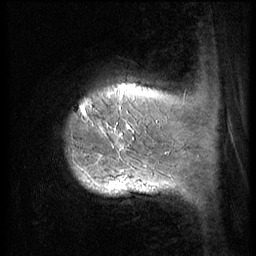
Breast MRI (dynamic contrast-enhanced), one sagittal slice; slice 8 of 56 in the series (ordered by position); 3 images stored at this slice position (order not interpretable as contrast timing); 1.5 T; TE 4.2 ms, TR 9 ms; 256 × 256 image matrix, field of view 180 × 180 mm. Patient: female, 49 years. From the clinical record (not read from this slice): setting: breast cancer imaged before/during neoadjuvant chemotherapy; receptor status: HER2-positive.
Structures marked on this image (semi-automatically segmented with operator editing):
- analysis volume of interest (the breast-tissue region the enhancement analysis was run in; not a lesion): box from (x=55, y=79) to (x=152, y=203) px
- tumour enhancement mask (voxels above the 140 % enhancement threshold inside the analysis volume of interest): (x=80, y=84)–(x=146, y=193)